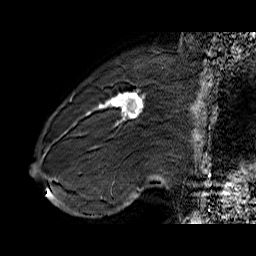
Breast MRI (dynamic contrast-enhanced), one sagittal slice; position 17 of 60 along the scan axis; dynamic contrast-enhanced series, time point 2 of 6 at this slice position (early post-contrast); 1.5 T; TE 6.4 ms, TR 32.9 ms; 4 mm slice thickness; 256 × 256 image matrix. Female patient. Case-level facts recorded for this patient, not image findings: setting: breast cancer imaged before/during neoadjuvant chemotherapy; receptor status: HER2-positive.
Annotated regions visible in this slice (semi-automatically segmented with operator editing):
- analysis volume of interest (the breast-tissue region the enhancement analysis was run in; not a lesion): bounding box (x1, y1, x2, y2) in pixels: (71, 80, 155, 146)
- tumour enhancement mask (voxels above the 100 % enhancement threshold inside the analysis volume of interest): (88, 91, 145, 124)